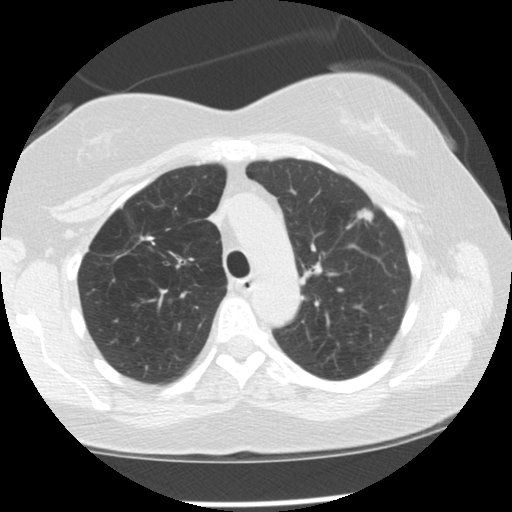
Low-dose screening chest CT, one axial slice; position 92 of 128 along the scan axis; reconstruction kernel STANDARD; 120 kVp; lung window (W 1500 / L -600 HU); 512 × 512 image matrix, field of view 319 × 319 mm.
Outlined on this slice (expert manual segmentation):
- lesion 1 (tumor, upper lobe of left lung): bounding box [x1, y1, x2, y2] px = [357, 208, 373, 222]